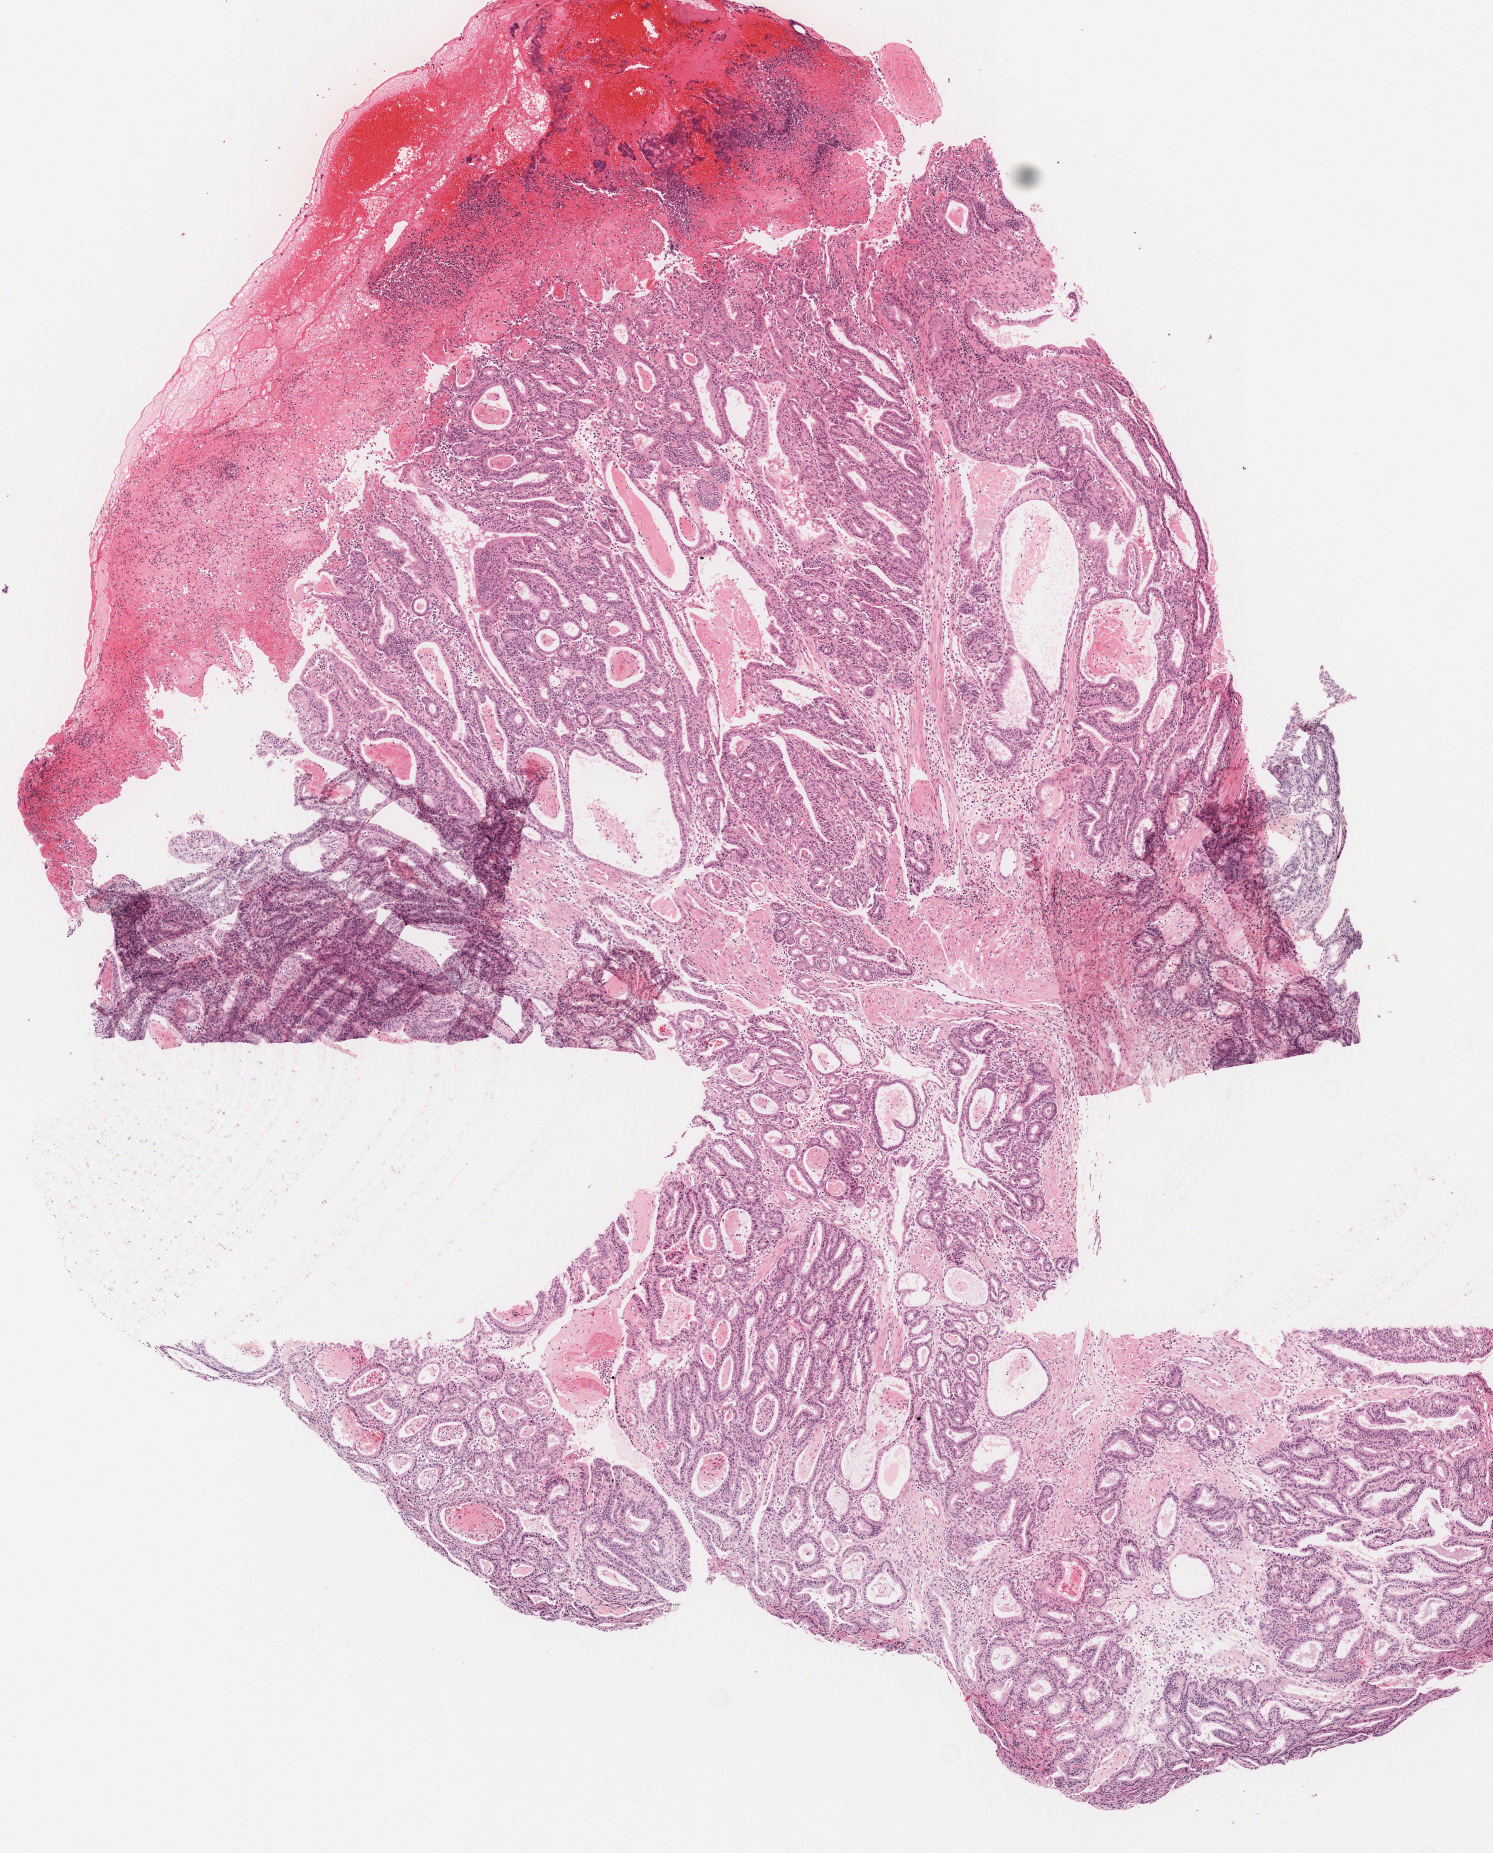
Digitized H&E tissue section (whole slide) — low-resolution overview of the scanned area, about 5.9 x 7.3 mm, formalin-fixed paraffin-embedded (FFPE) diagnostic section, sample: primary tumour, stomach. Male patient; age at initial diagnosis 75 years. Histologic grade: G2 (moderately differentiated).
• lymph nodes positive (case pathology): 0 of 79 examined
• AJCC pathologic stage: IA
• diagnosis: Tubular adenocarcinoma (body of stomach)
• TNM: T1b N0 M0